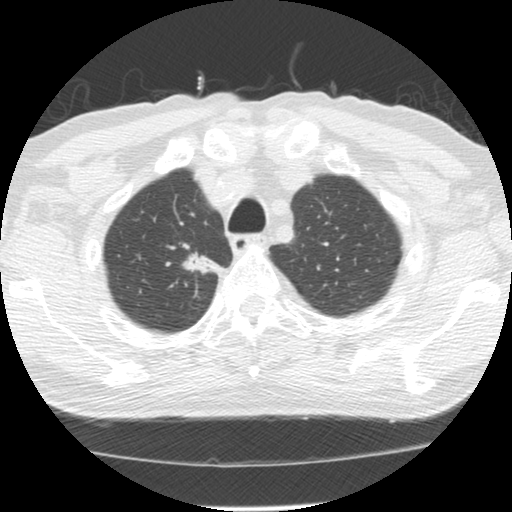
Low-dose screening chest CT, axial slice. Baseline screening round. Lung window (W 1500 / L -600 HU). 120 kVp. Male, age 64 years at enrolment. Former smoker at enrolment.
- Lesion marked by an expert reader, bounding box <177,238,224,279> (left, top, right, bottom; pixels).
- The exam's reader record, not a measurement of the box and not confirmed to be the same lesion: non-calcified nodule or mass ≥4 mm, right upper lobe, 20 × 13 mm, spiculated (stellate) margins, soft tissue attenuation.